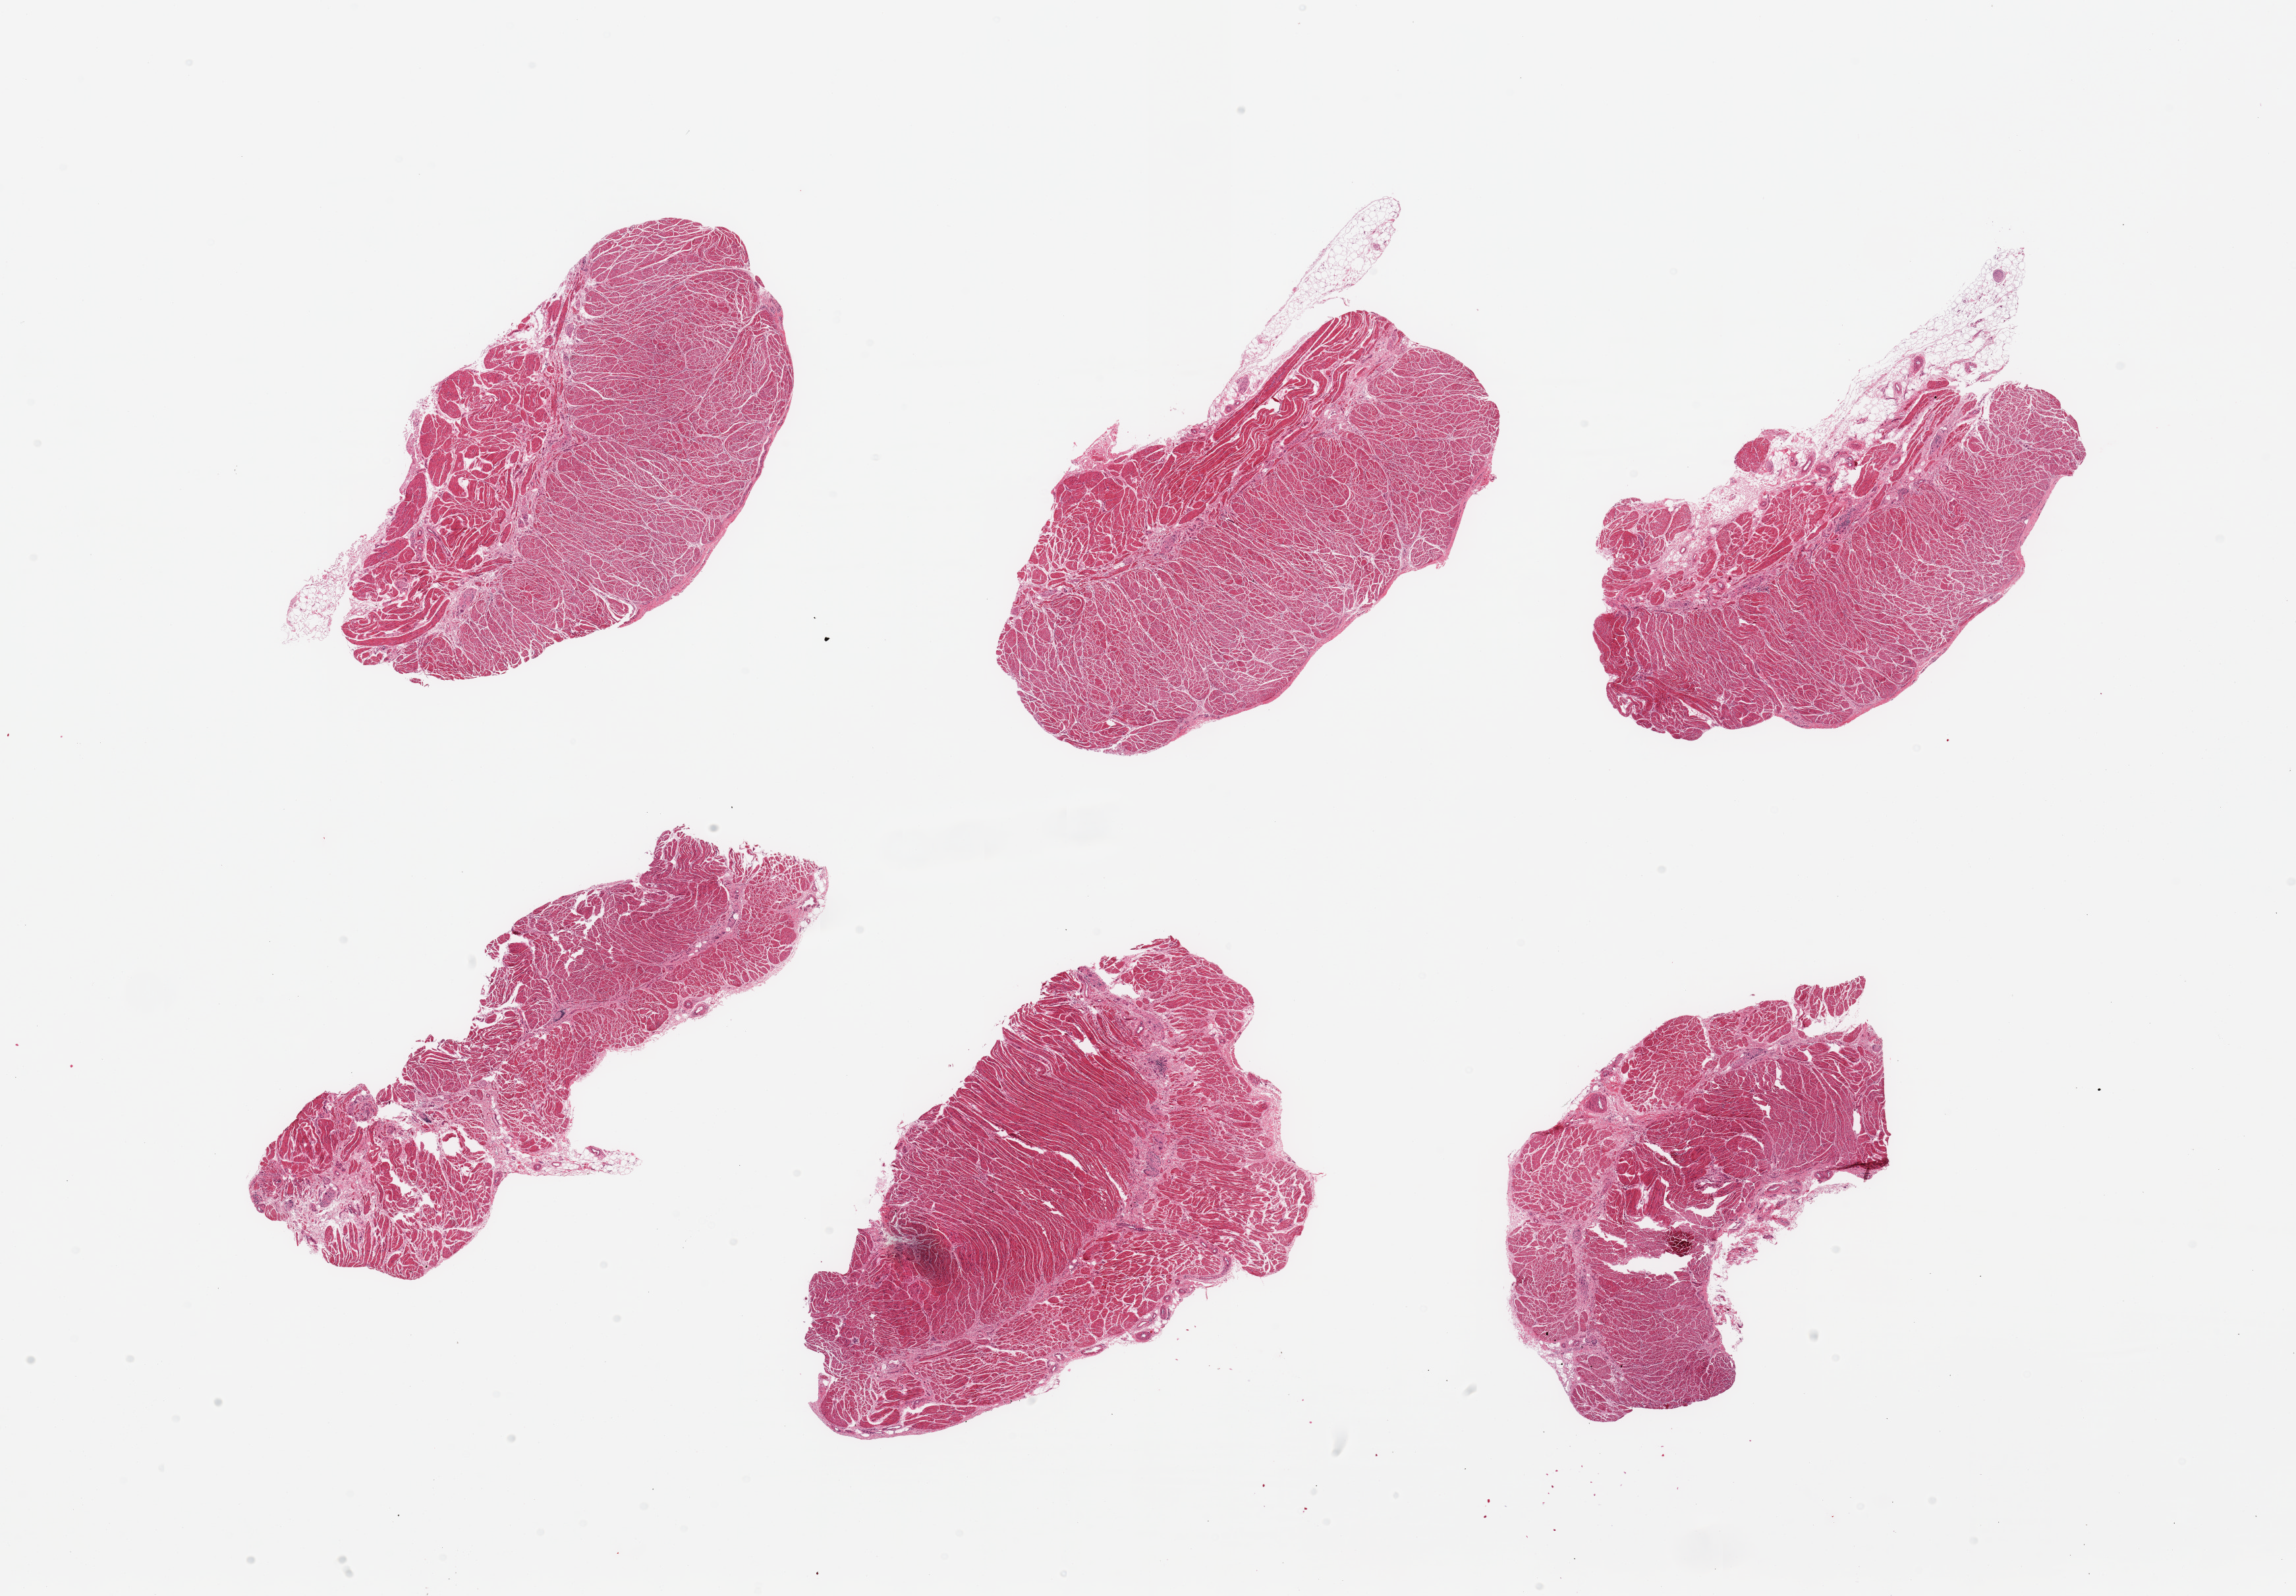
Digitized haematoxylin and eosin-stained section, brightfield — low-resolution overview of the scanned area, about 27.6 x 19.2 mm (from a 20x scan); PAXgene-fixed paraffin-embedded (PFPE) section; sampled site (target tissue): gastroesophageal junction; donor tissue sample. Male donor.
Pathologist's review note for this sample: 6 pieces, confirmed target muscularis.